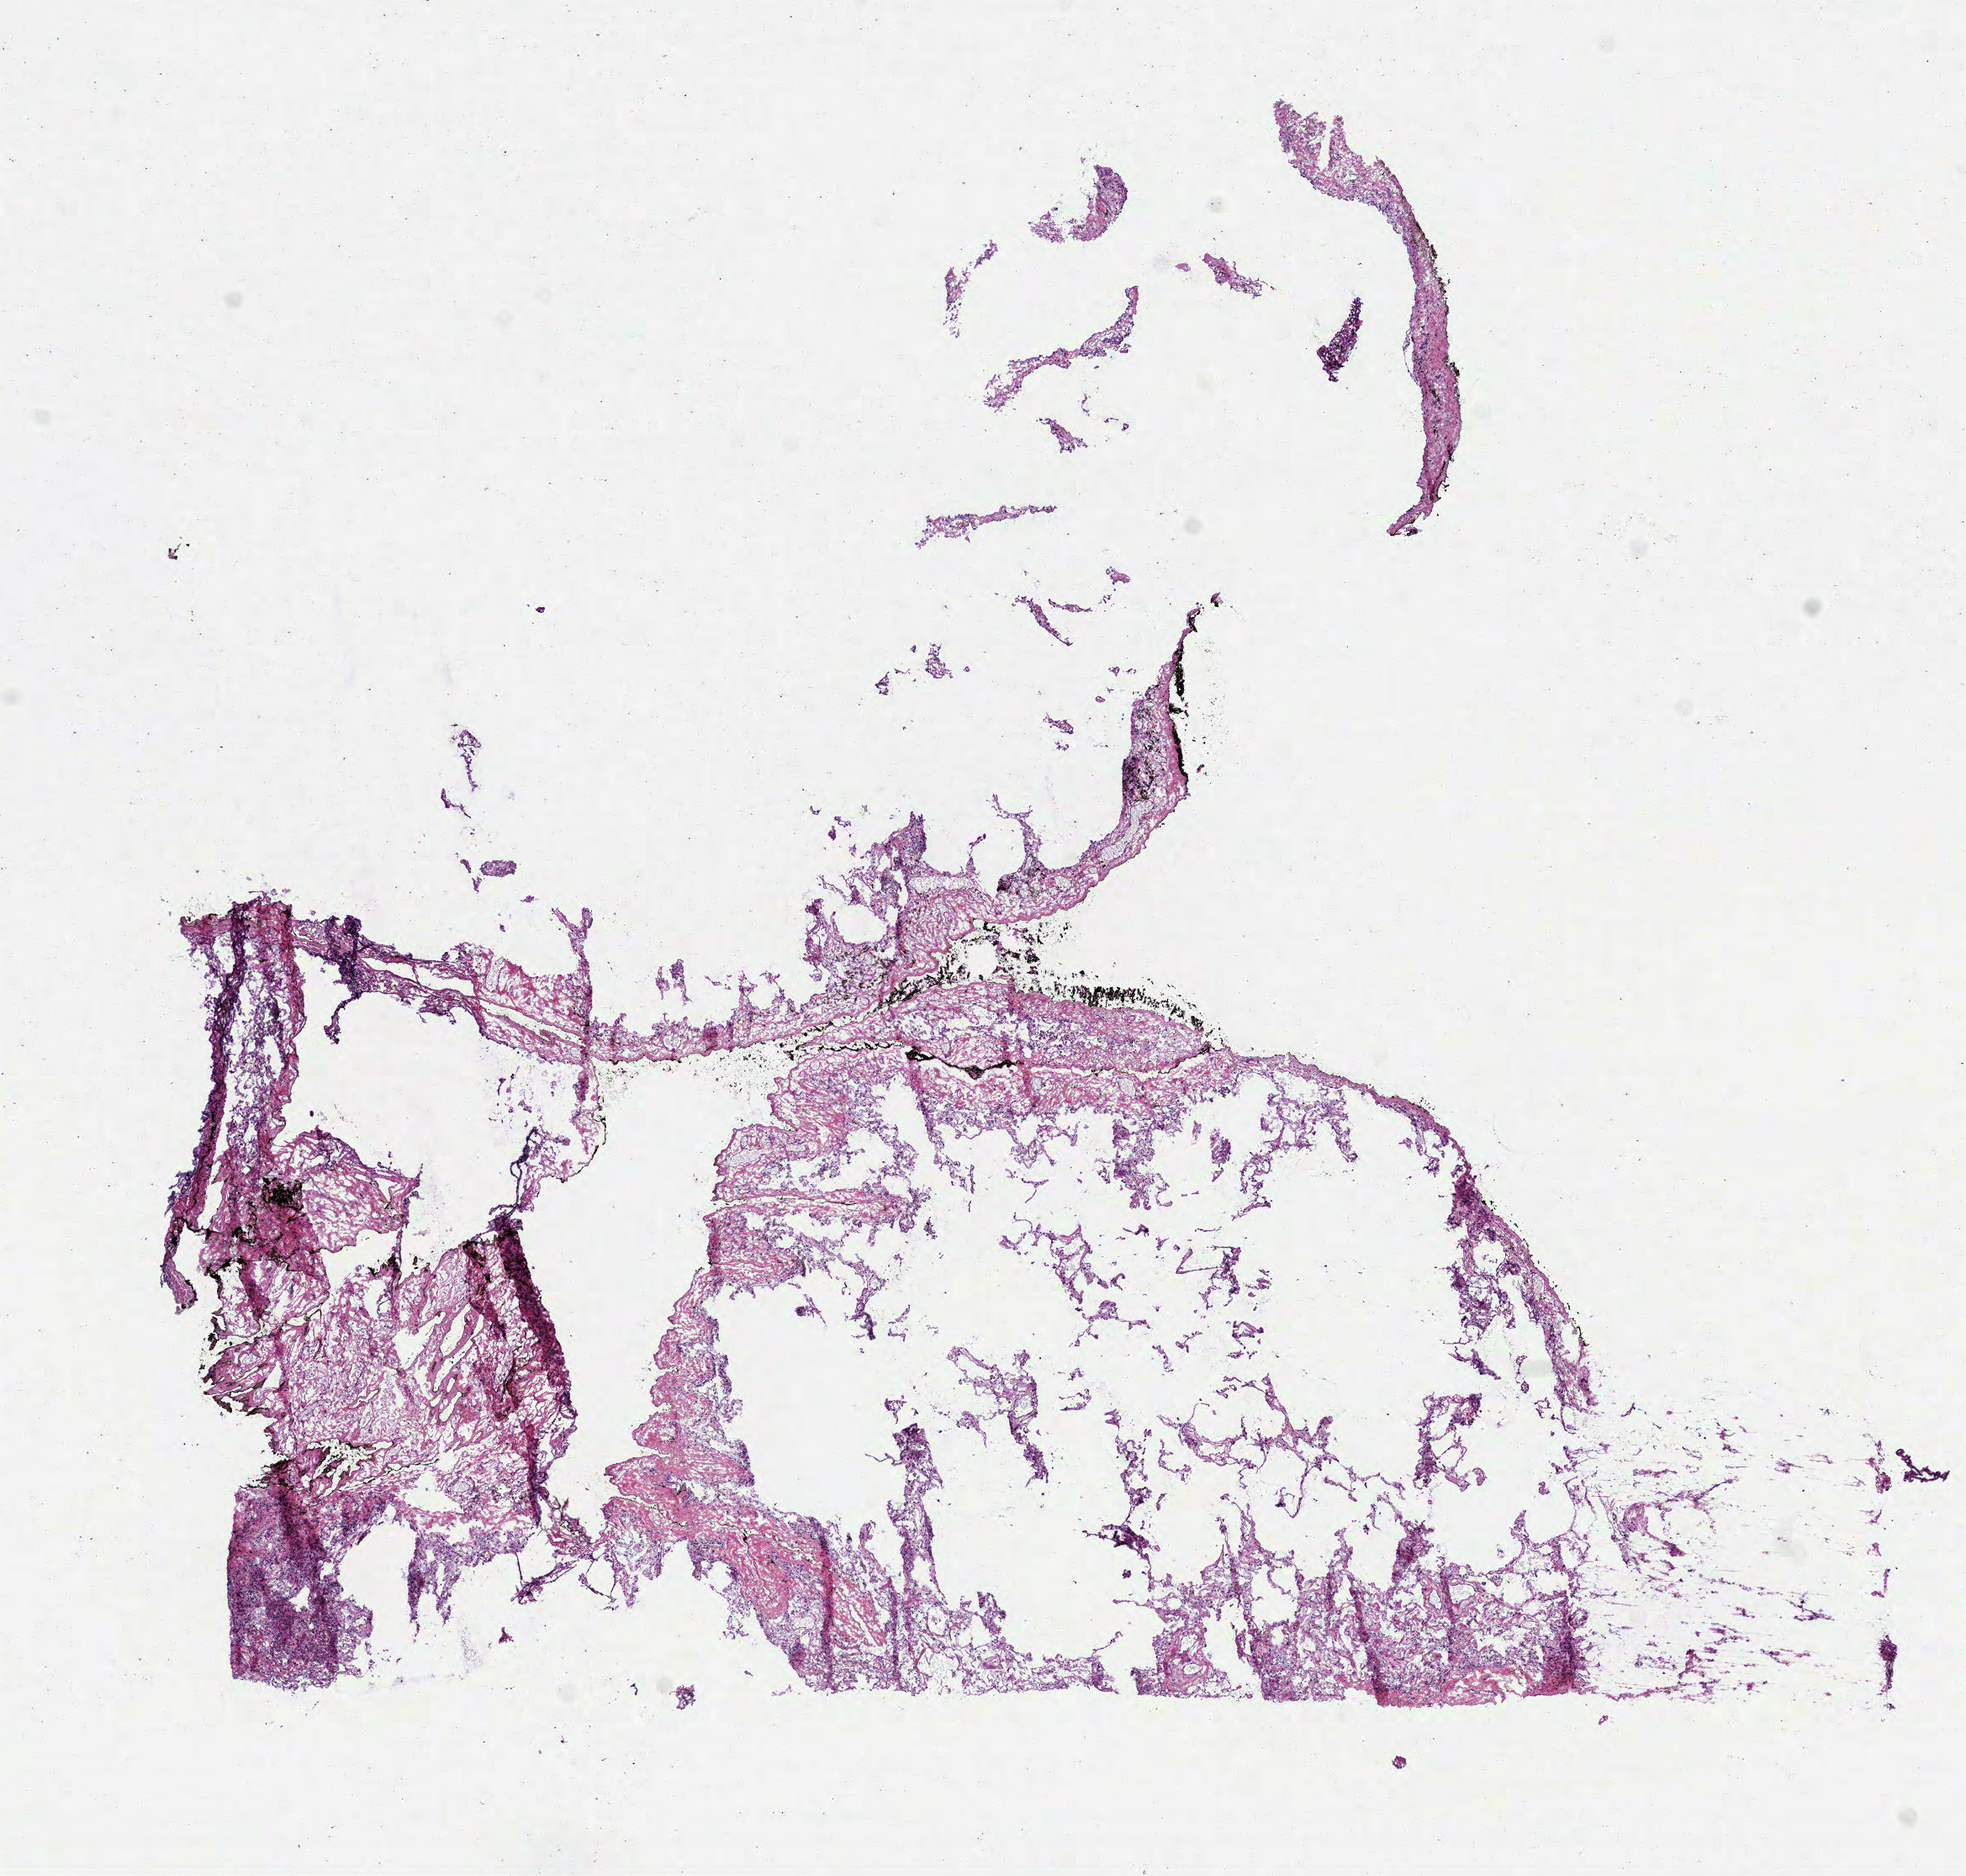
Digitized Hematoxylin and eosin (H&E) stained tissue section (whole slide) — shown as a low-resolution overview of the whole scanned area (about 9.4 x 9.0 mm, from a 40x scan); frozen section from the top of the tissue portion; sample: solid tissue normal (non-tumour tissue), lung. Male patient; age at initial diagnosis 81 years.
This section: solid tissue normal (non-tumour) sample from the same patient. Patient diagnosis: Adenocarcinoma, NOS (upper lobe, lung).